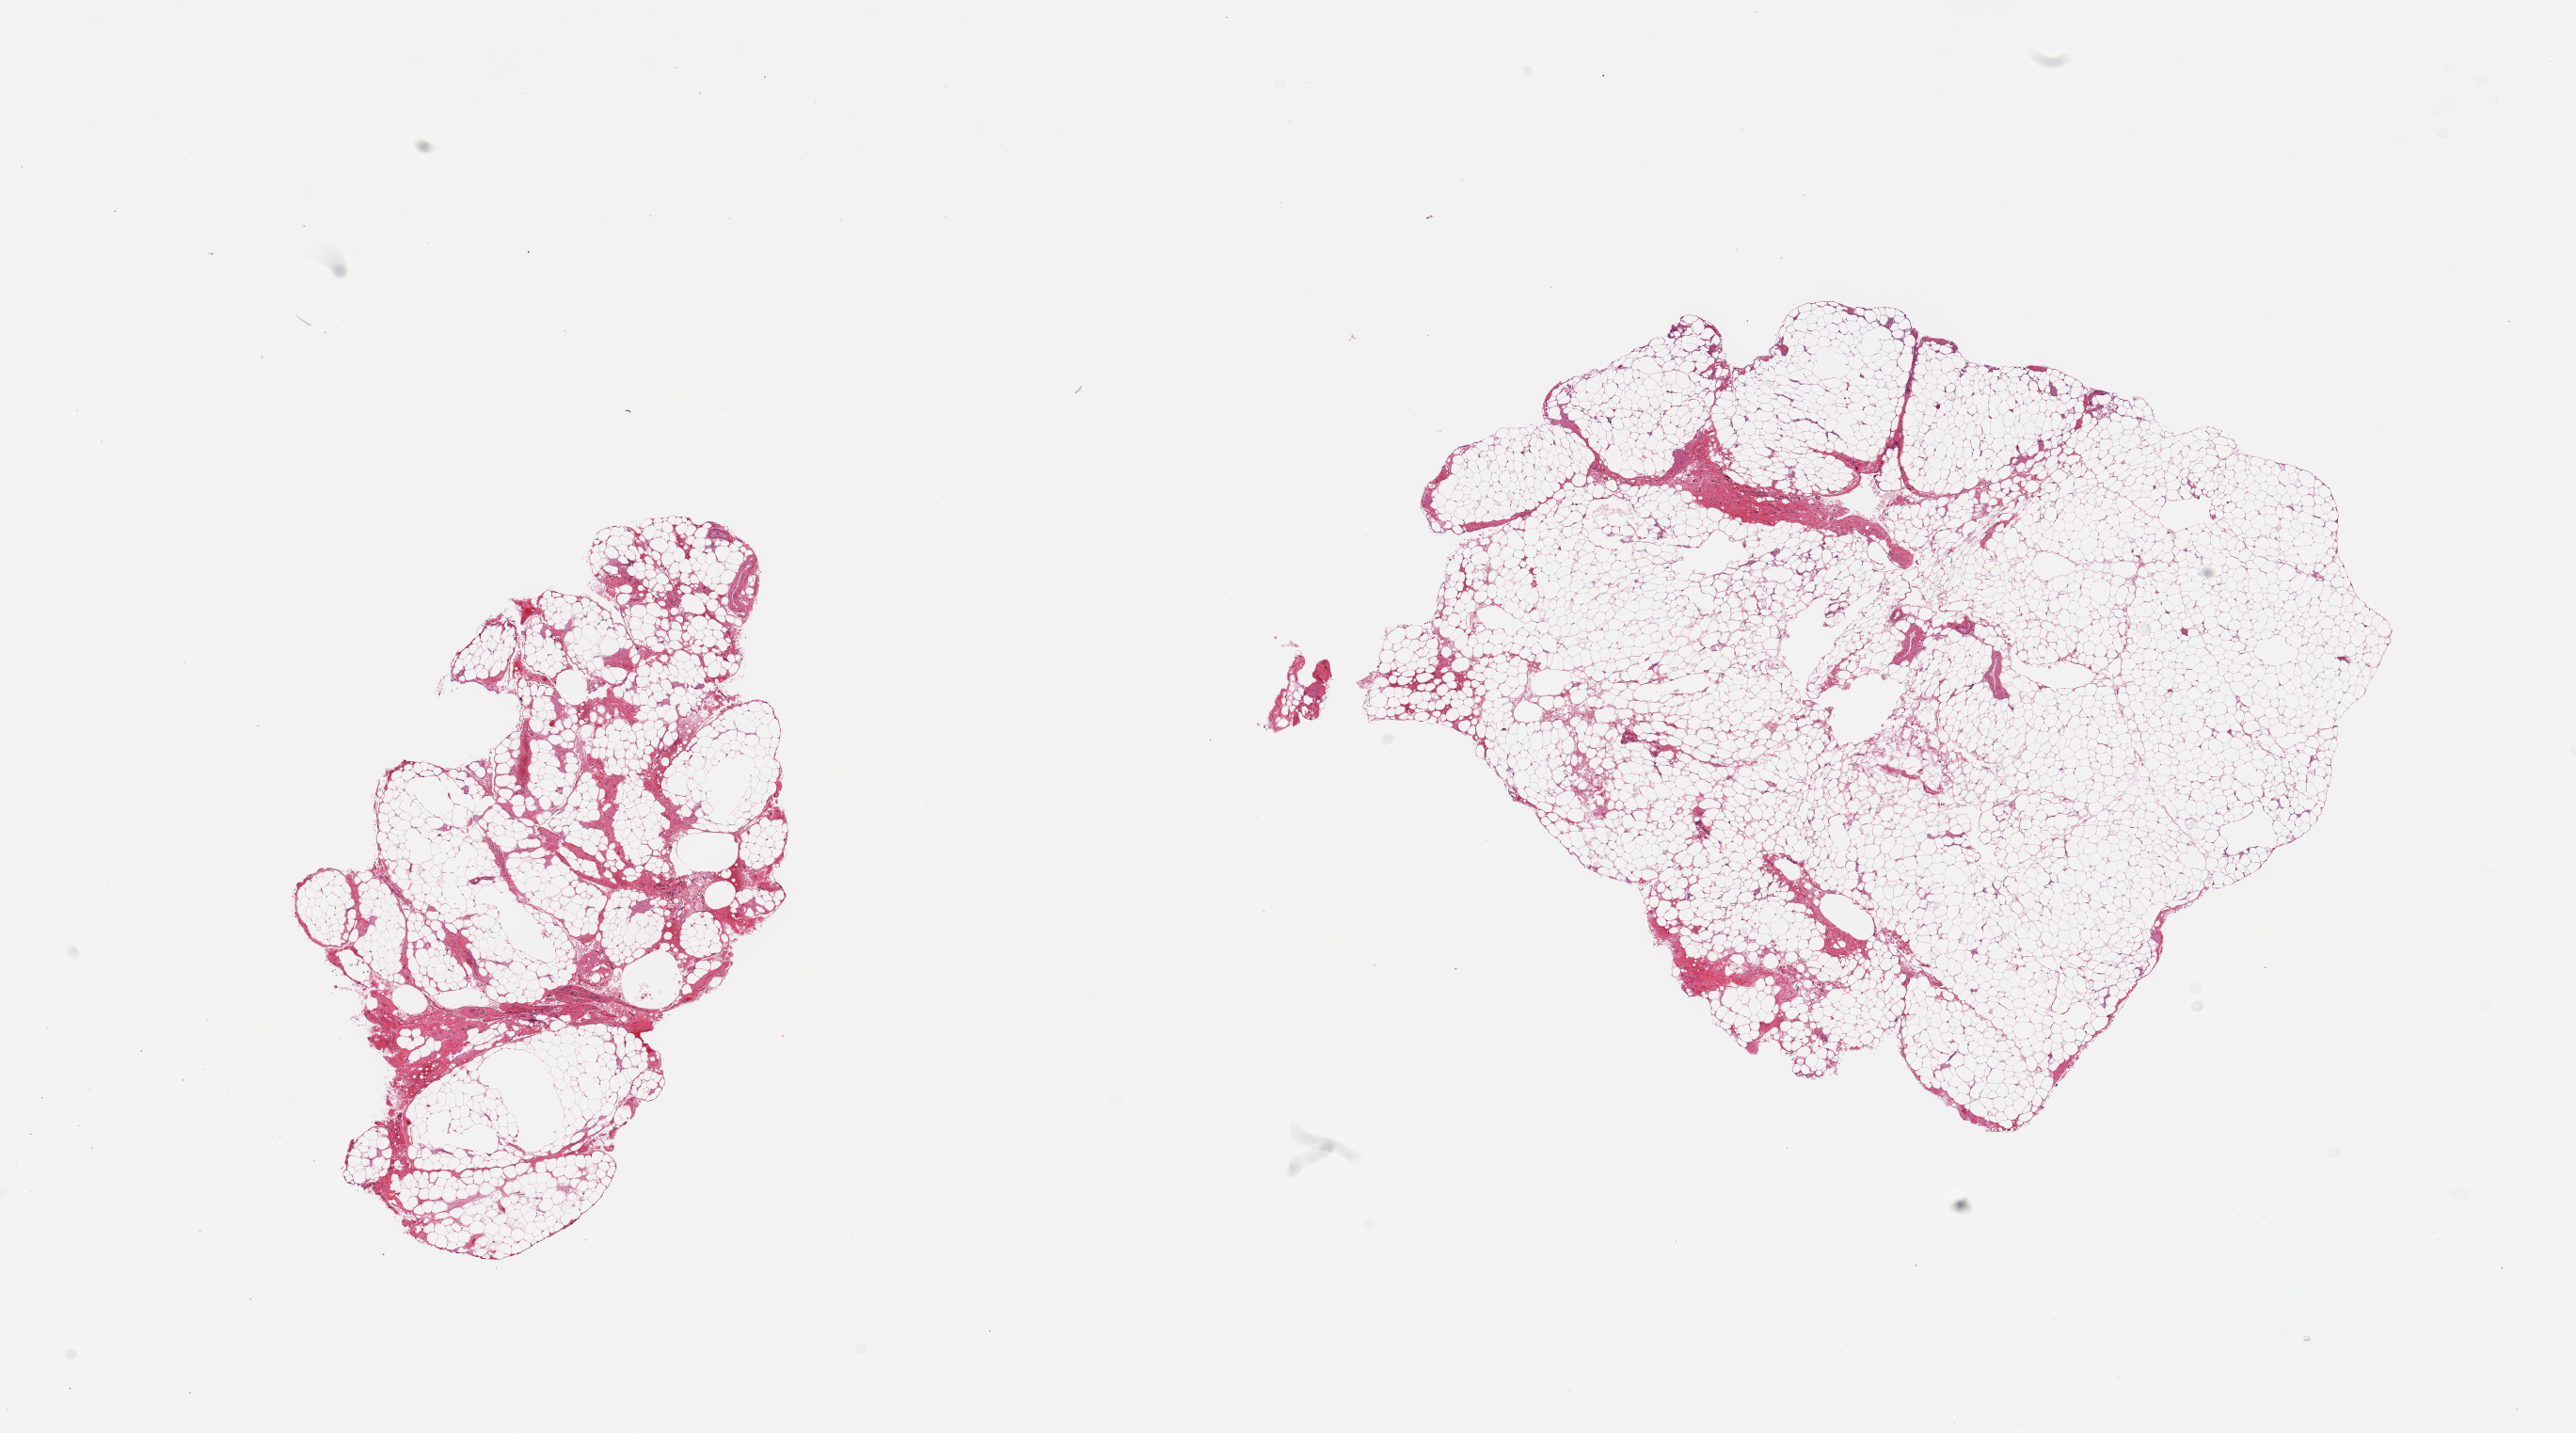
Haematoxylin and eosin whole-slide image, brightfield — low-resolution overview of the scanned area, about 21.7 x 12.0 mm. PAXgene-fixed, paraffin-embedded tissue. Sampled site (target tissue): omentum. Donor tissue sample. Male donor.
• review note (as recorded): 2 pieces; 10% & 5 % fibrous content